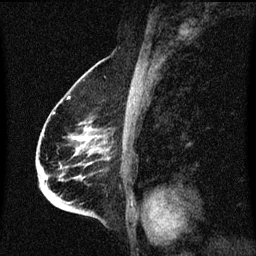
Breast MRI (dynamic contrast-enhanced), one sagittal slice; slice 40 of 60 in the series (ordered by position); dynamic contrast-enhanced series, image 2 of 3 at this slice position (ordered by acquisition); 1.5 T; TE 4.2 ms, TR 8.4 ms; 2 mm slice thickness; 256 × 256 image matrix, field of view 200 × 200 mm. Patient: female, 68 years. Case-level facts recorded for this patient, not image findings: setting: breast cancer imaged before/during neoadjuvant chemotherapy; receptor status: triple-negative.
Outlined on this slice (semi-automatic segmentation, software-assisted and operator-edited):
- analysis volume of interest (the breast-tissue region the enhancement analysis was run in; not a lesion): bounding box (x1, y1, x2, y2) in pixels: (38, 96, 113, 213)
- tumour enhancement mask (voxels above the 70 % enhancement threshold inside the analysis volume of interest): (68, 138, 100, 205)